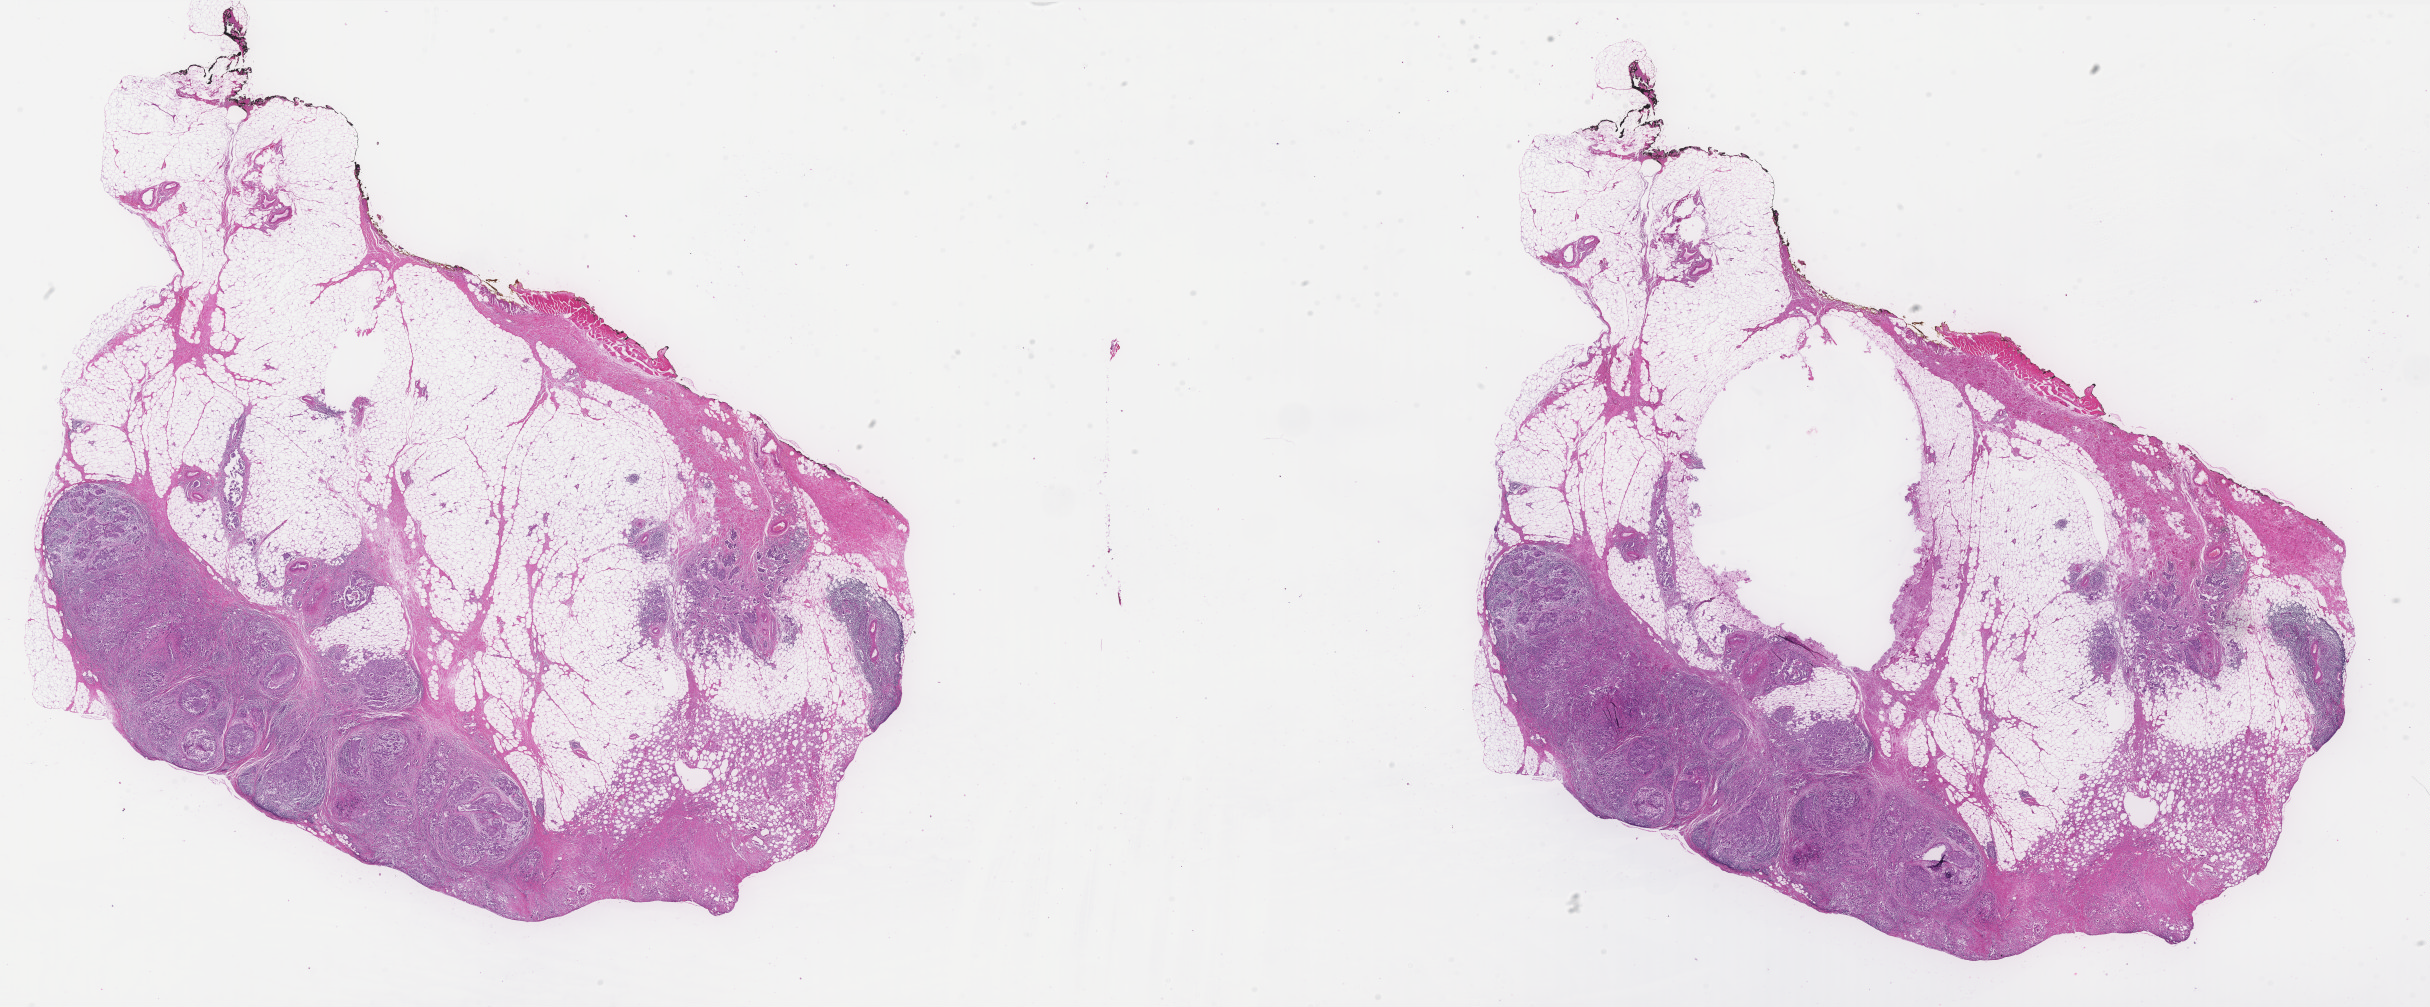
Digitized H&E tissue section (whole slide) — whole scanned area (about 39.0 x 16.1 mm, from a 40x scan) shown as a low-resolution overview; FFPE section; breast, primary tumour sample. Patient: female, age at initial diagnosis 36 years.
• lymph nodes positive (case pathology): 18 of 20 examined
• diagnosis: Infiltrating duct carcinoma, NOS
• laterality: left
• AJCC pathologic stage: IIIC (6th edition)